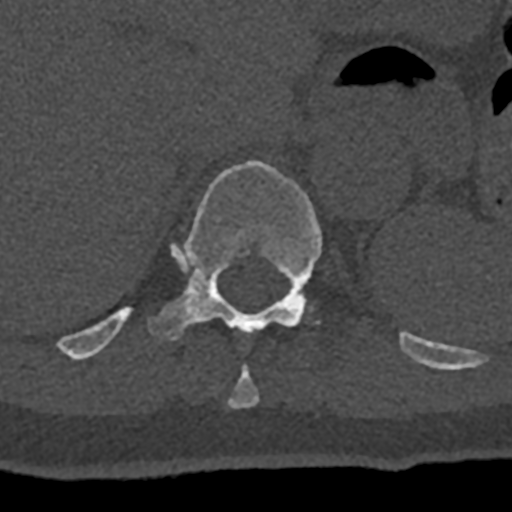
CT including the spine, one axial slice; position 550 of 797 along the scan axis; reconstruction kernel Br40s/3; bone window (W 1800 / L 400 HU); 0.5 mm slice thickness; 512 × 512 image matrix, field of view 160 × 160 mm. Male patient, age 74 years. From the clinical record (not read from this slice): primary cancer: renal.
Structures marked on this image (semi-automatically segmented with operator editing):
- T10 vertebra: bounding box (x1, y1, x2, y2) in pixels: (228, 364, 260, 409)
- T11 vertebra: (70, 161, 432, 367)